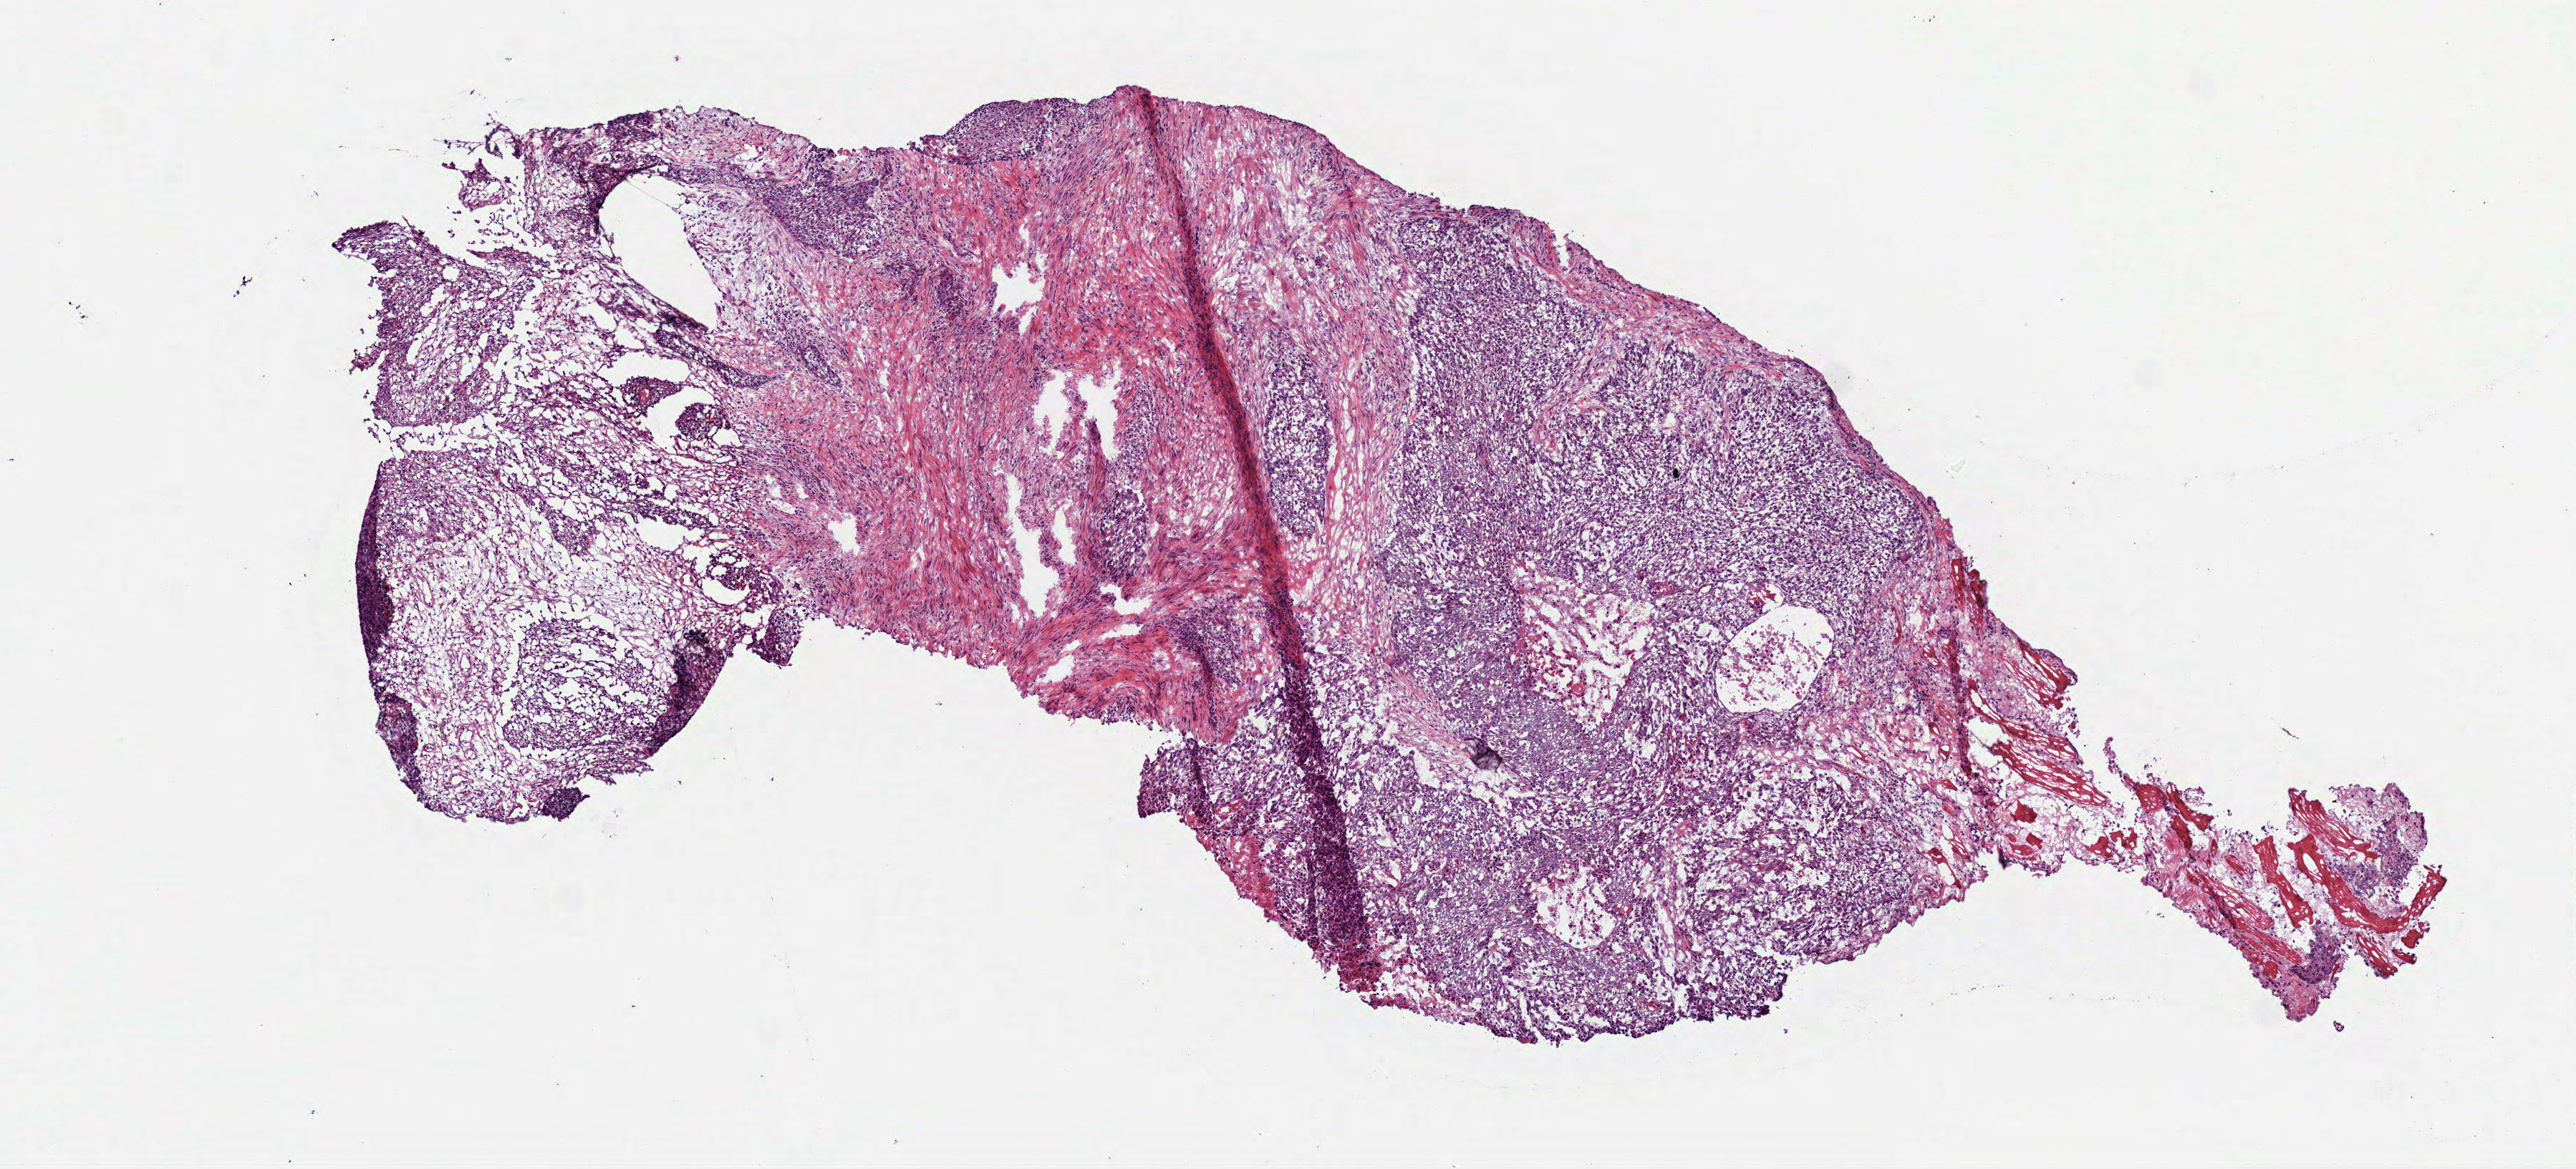
Digitized H&E tissue section (whole slide), a low-resolution overview of the entire scanned area, about 7.3 x 3.3 mm; frozen section; head and neck, primary tumour sample. Male, age 82 years at initial diagnosis.
Histologic diagnosis: Squamous cell carcinoma, NOS (overlapping lesion of lip, oral cavity and pharynx).